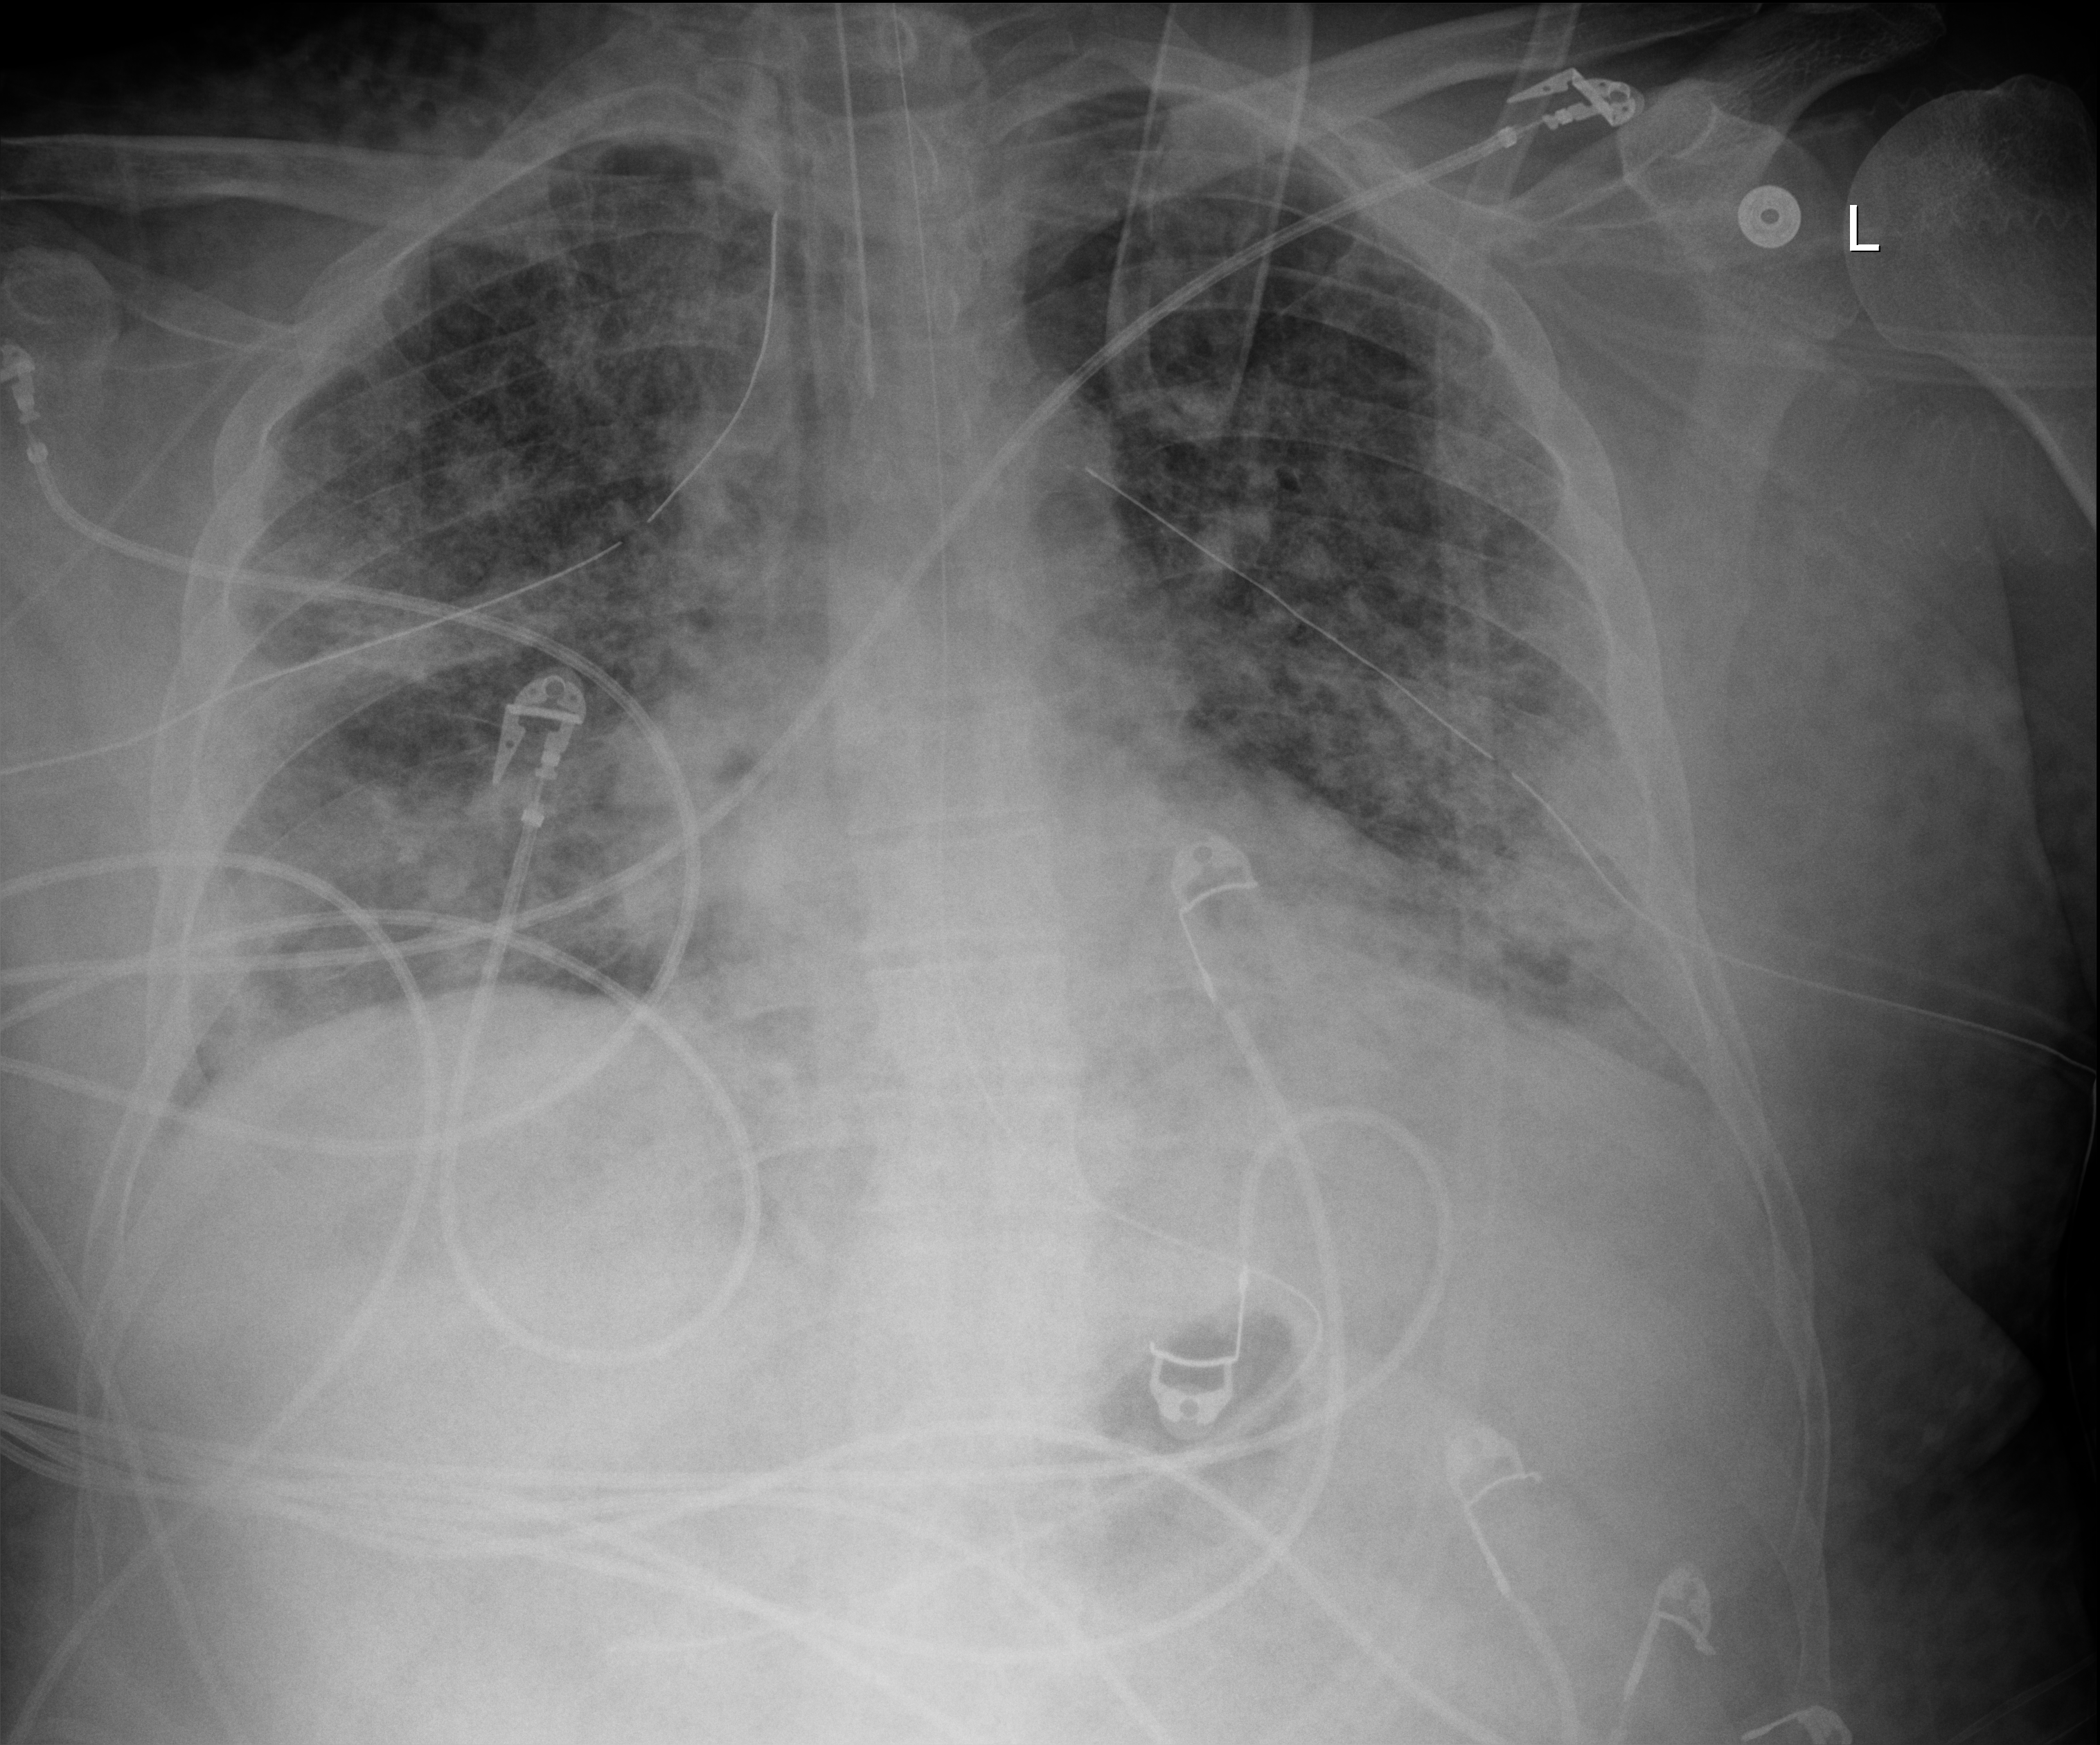
Chest radiograph (digital radiography), anteroposterior (AP) projection. Patient hospitalised with COVID-19; male, aged 18–59 years.
Admission-level facts for this patient (not findings on this image; timing relative to this image not recorded): admitted to intensive care during this hospital stay: yes.